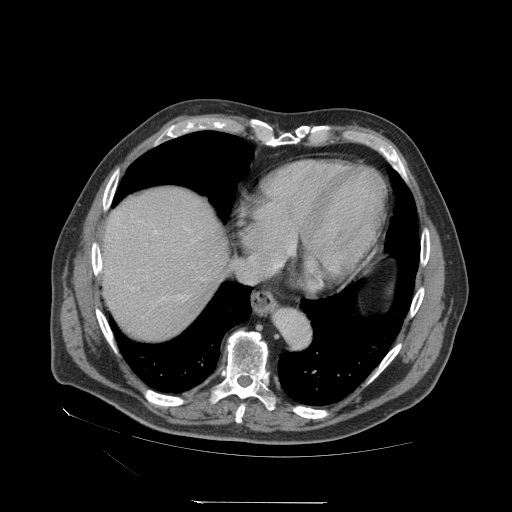
Contrast-enhanced abdominal CT (liver protocol), one axial slice; reconstruction kernel STANDARD; 140 kVp; soft-tissue window (W 400 / L 40 HU); 2.5 mm slice thickness; 512 × 512 image matrix, field of view 460 × 460 mm. Case-level facts recorded for this patient, not image findings: diagnosis: hepatocellular carcinoma (patient treated with transarterial chemoembolisation; whether this scan precedes or follows treatment is not stated here); TNM stage (as recorded): Stage-I; Child-Pugh class: A; tumour differentiation: well differentiated; tumour nodularity: uninodular.
Outlined on this slice (semi-automatically segmented with operator editing):
- abdominal aorta: box from (x=274, y=309) to (x=310, y=346) px
- liver parenchyma outside the tumour (the mass and vessels are separate outlines, so this box may not span the whole liver): (x=102, y=188)–(x=226, y=338)
- liver vessels: (x=155, y=231)–(x=184, y=299)